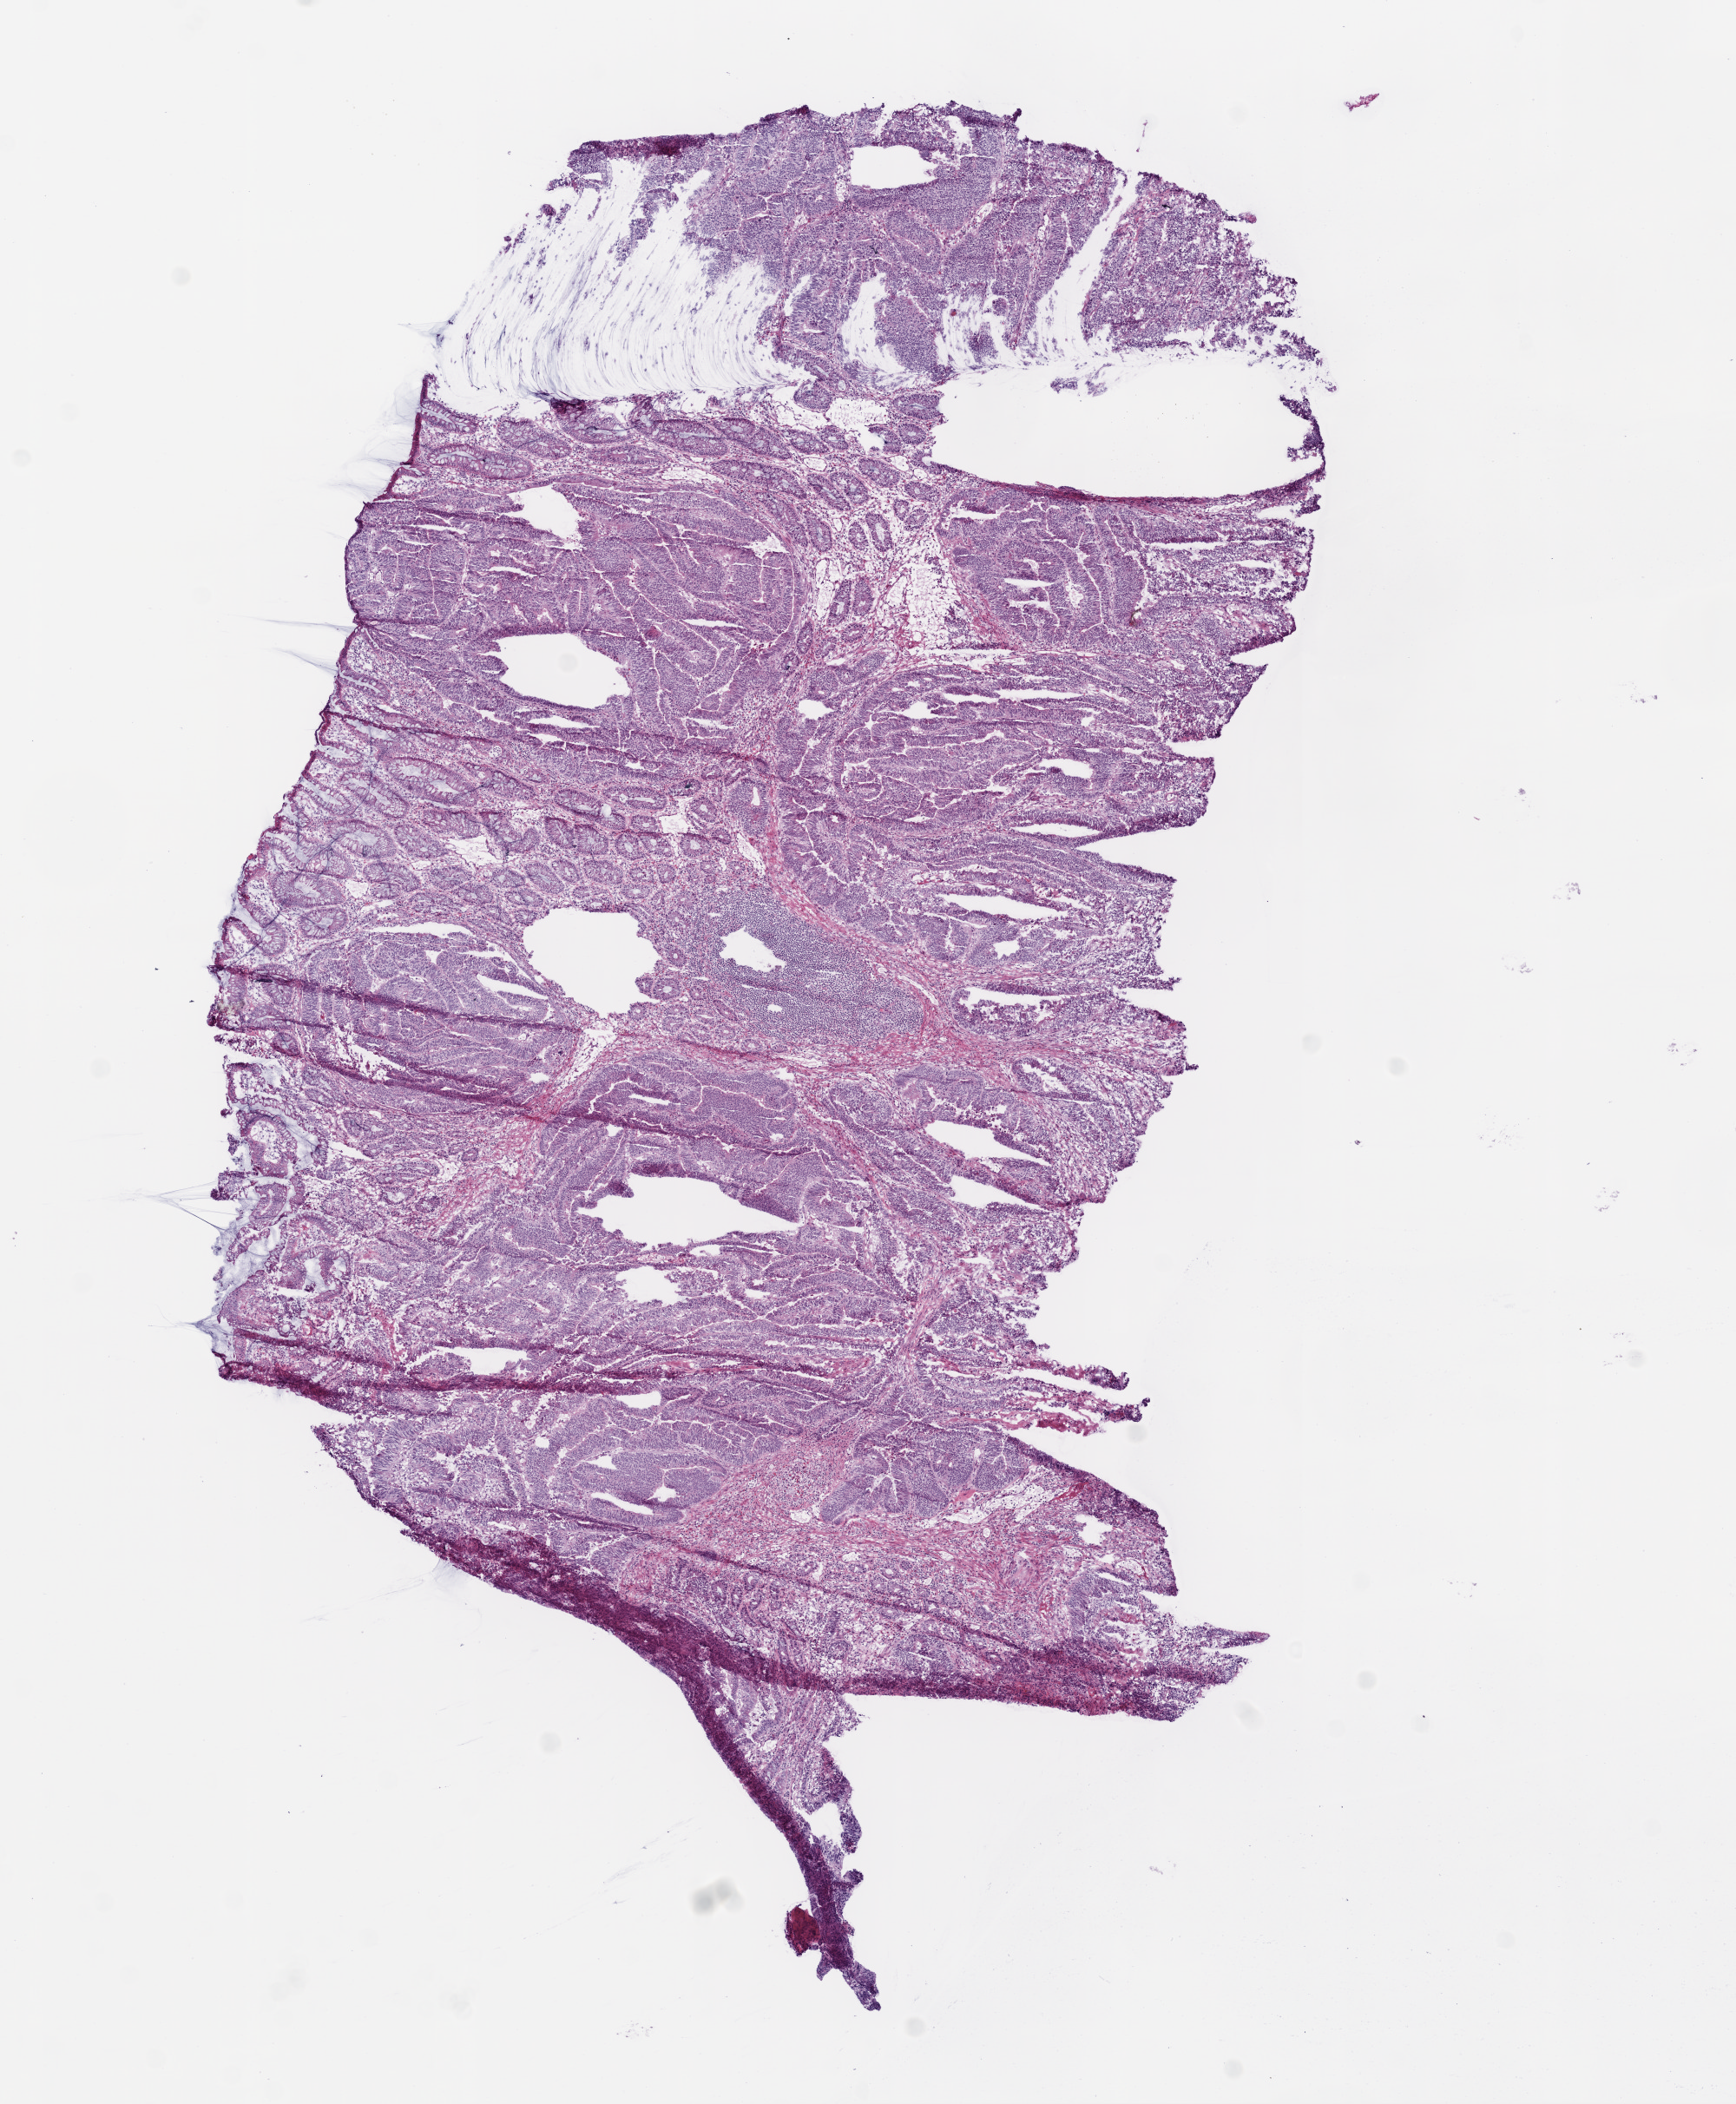
Whole-slide histology image, H&E — a low-resolution overview of the entire scanned area, about 8.0 x 9.7 mm (slide scanned at 20x), frozen section, primary tumour sample from the colon. Patient: female, age at initial diagnosis 41 years. Pathologist review of this section (percent, as recorded): tumour cells 80%, tumour nuclei 80%, normal cells 5%, stromal cells 10%, necrosis 5%.
* diagnosis: Adenocarcinoma, NOS
* AJCC pathologic stage: IIA
* lymph nodes positive (case pathology): 0 of 14 examined